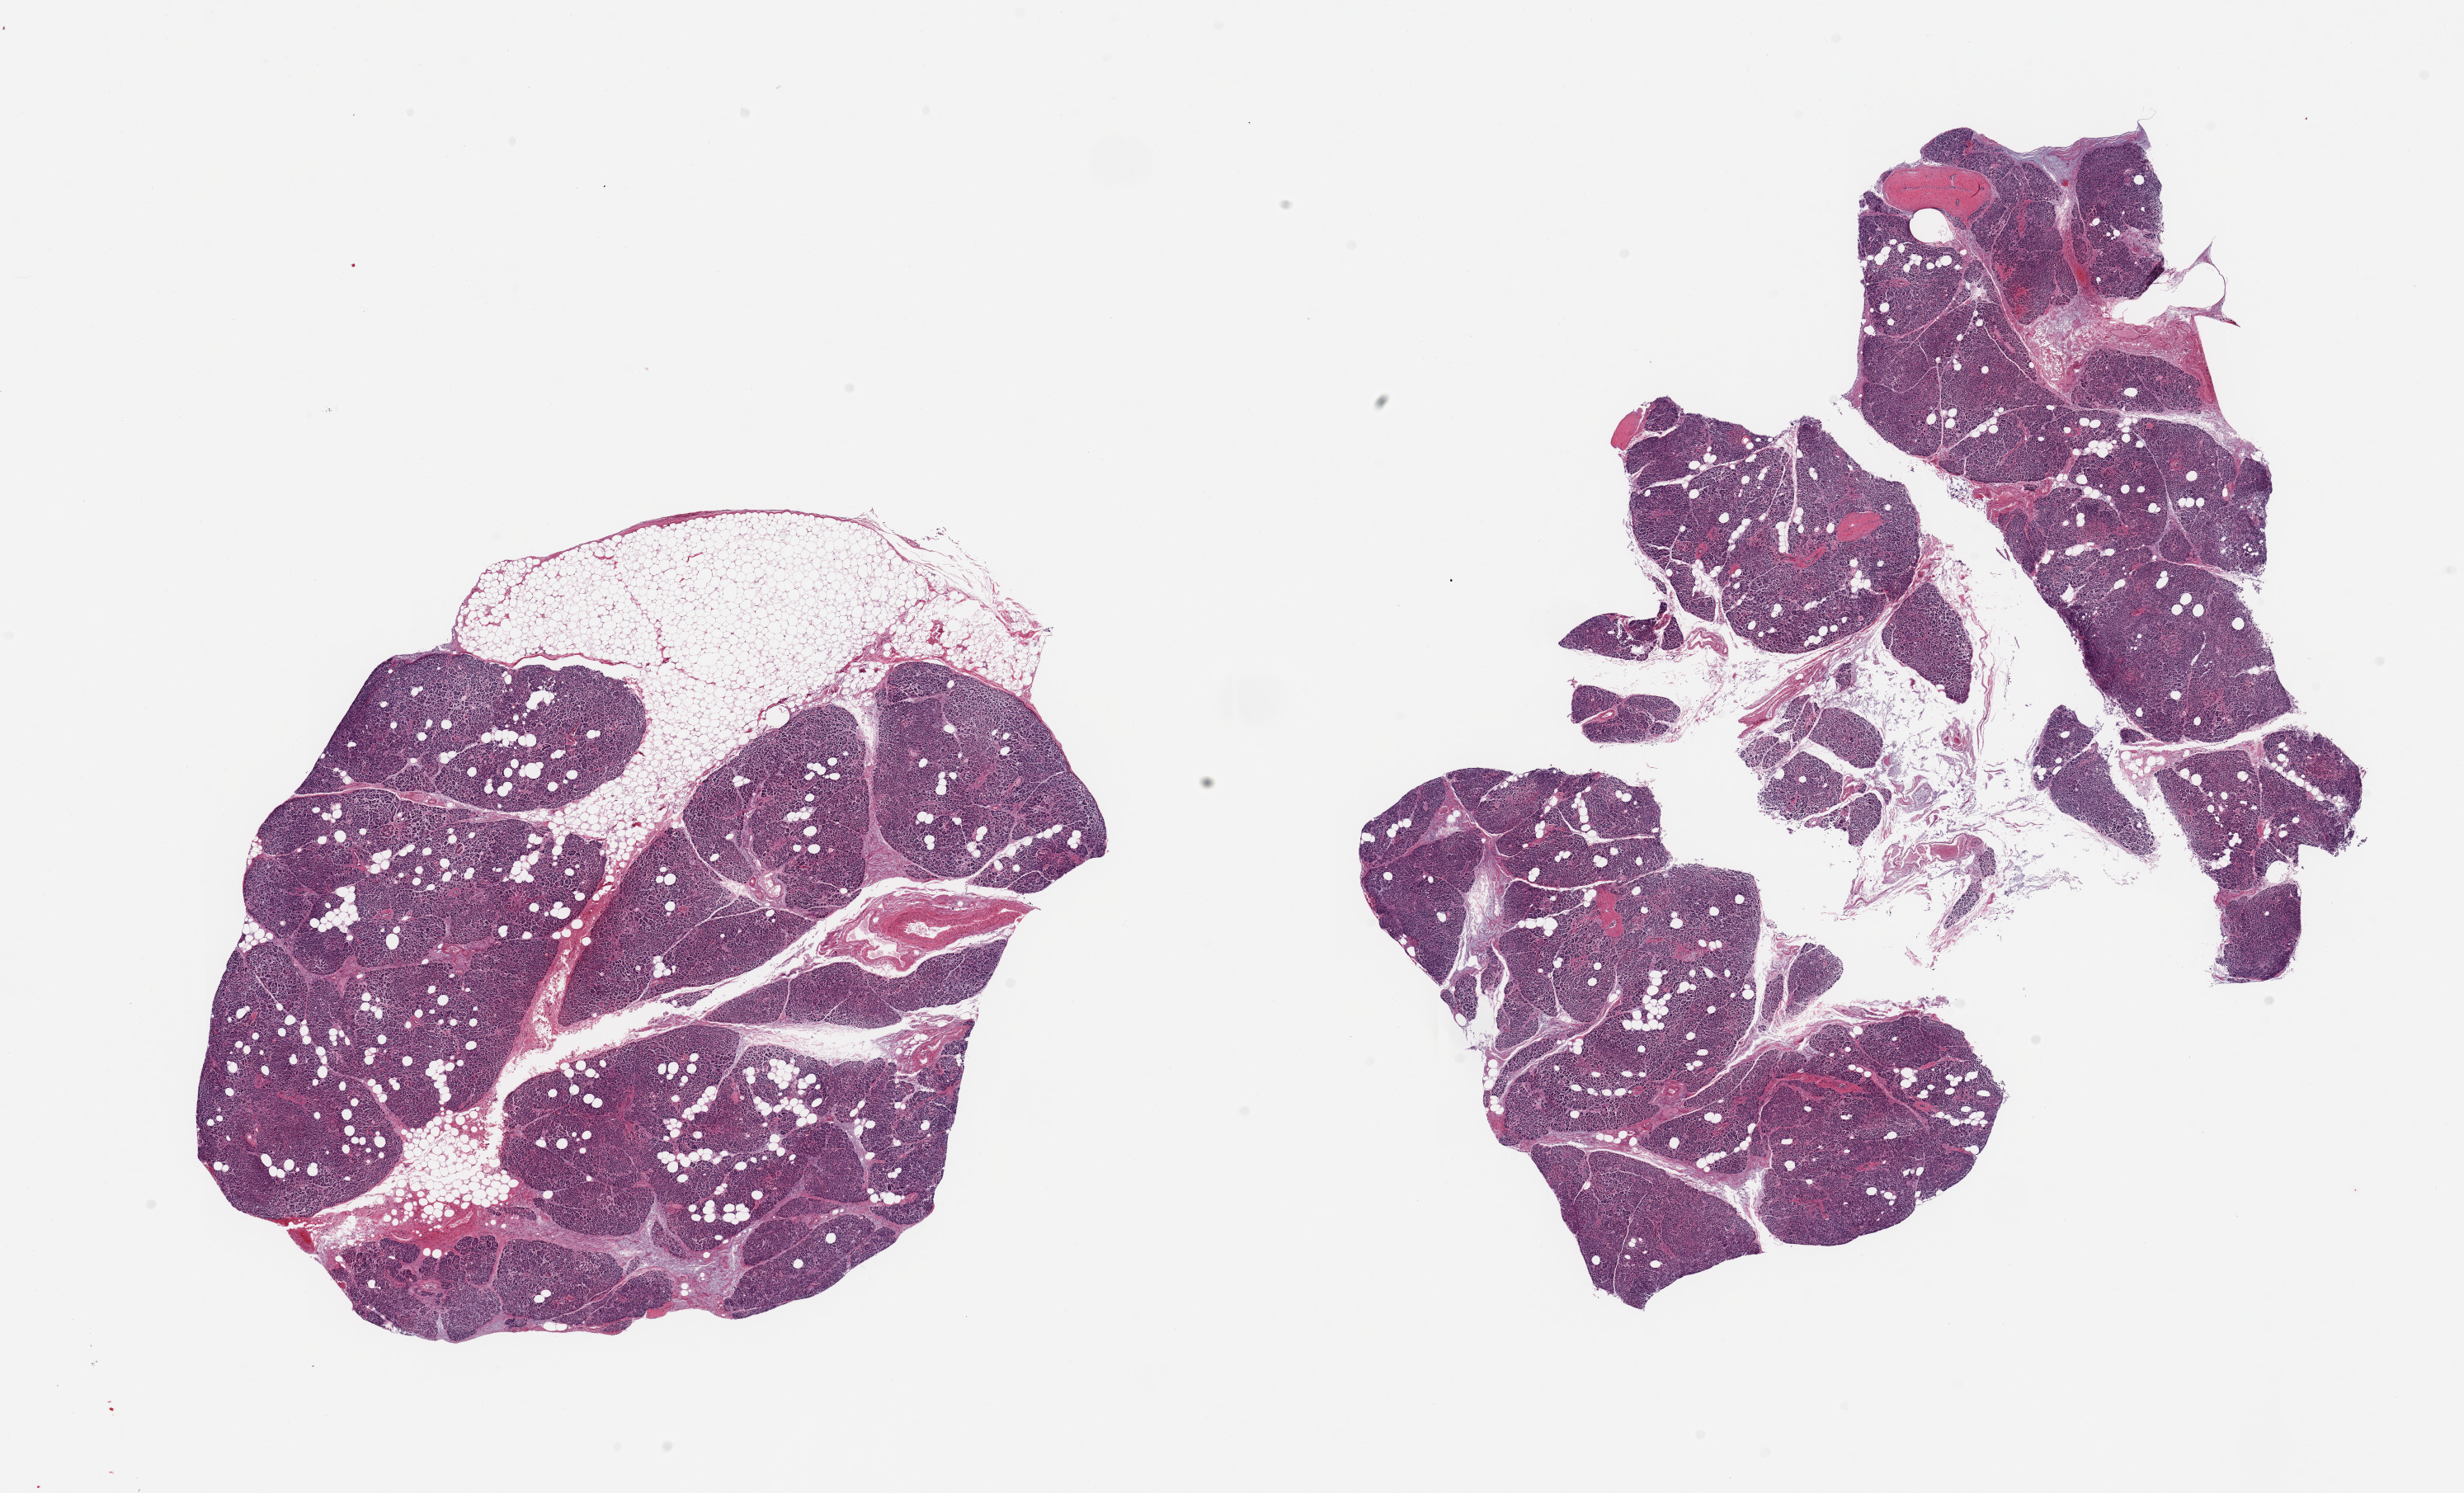
Whole-slide image, H&E stain — a low-resolution overview of the entire scanned area, about 23.6 x 14.3 mm (acquisition: 20x scan). PAXgene-fixed, paraffin-embedded tissue. Sampled site (target tissue): pancreas. Tissue donor sample. Female donor.
Review note (as recorded): 2 pieces; 30 & 10% external & internalfat.